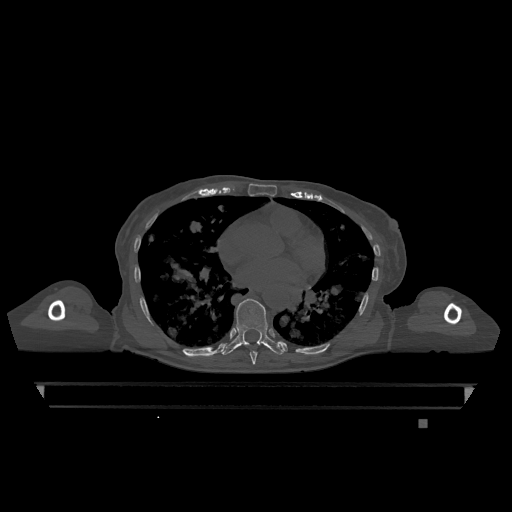
CT including the spine, one axial slice. Slice 705 of 1317 in the series (ordered by position). Bone window (W 1800 / L 400 HU). 0.5 mm slice thickness. 512 × 512 image matrix, field of view 500 × 500 mm. Female patient, age 74 years. Case-level facts recorded for this patient, not image findings: primary cancer: lung; vertebrae with lytic lesions (as recorded): T1, T4, T5, T6, L4, L5.
Structures marked on this image (semi-automatic segmentation, software-assisted and operator-edited):
- T7 vertebra: bounding box <250,351,257,365> (left, top, right, bottom; pixels)
- T9 vertebra: <222,299,284,355>